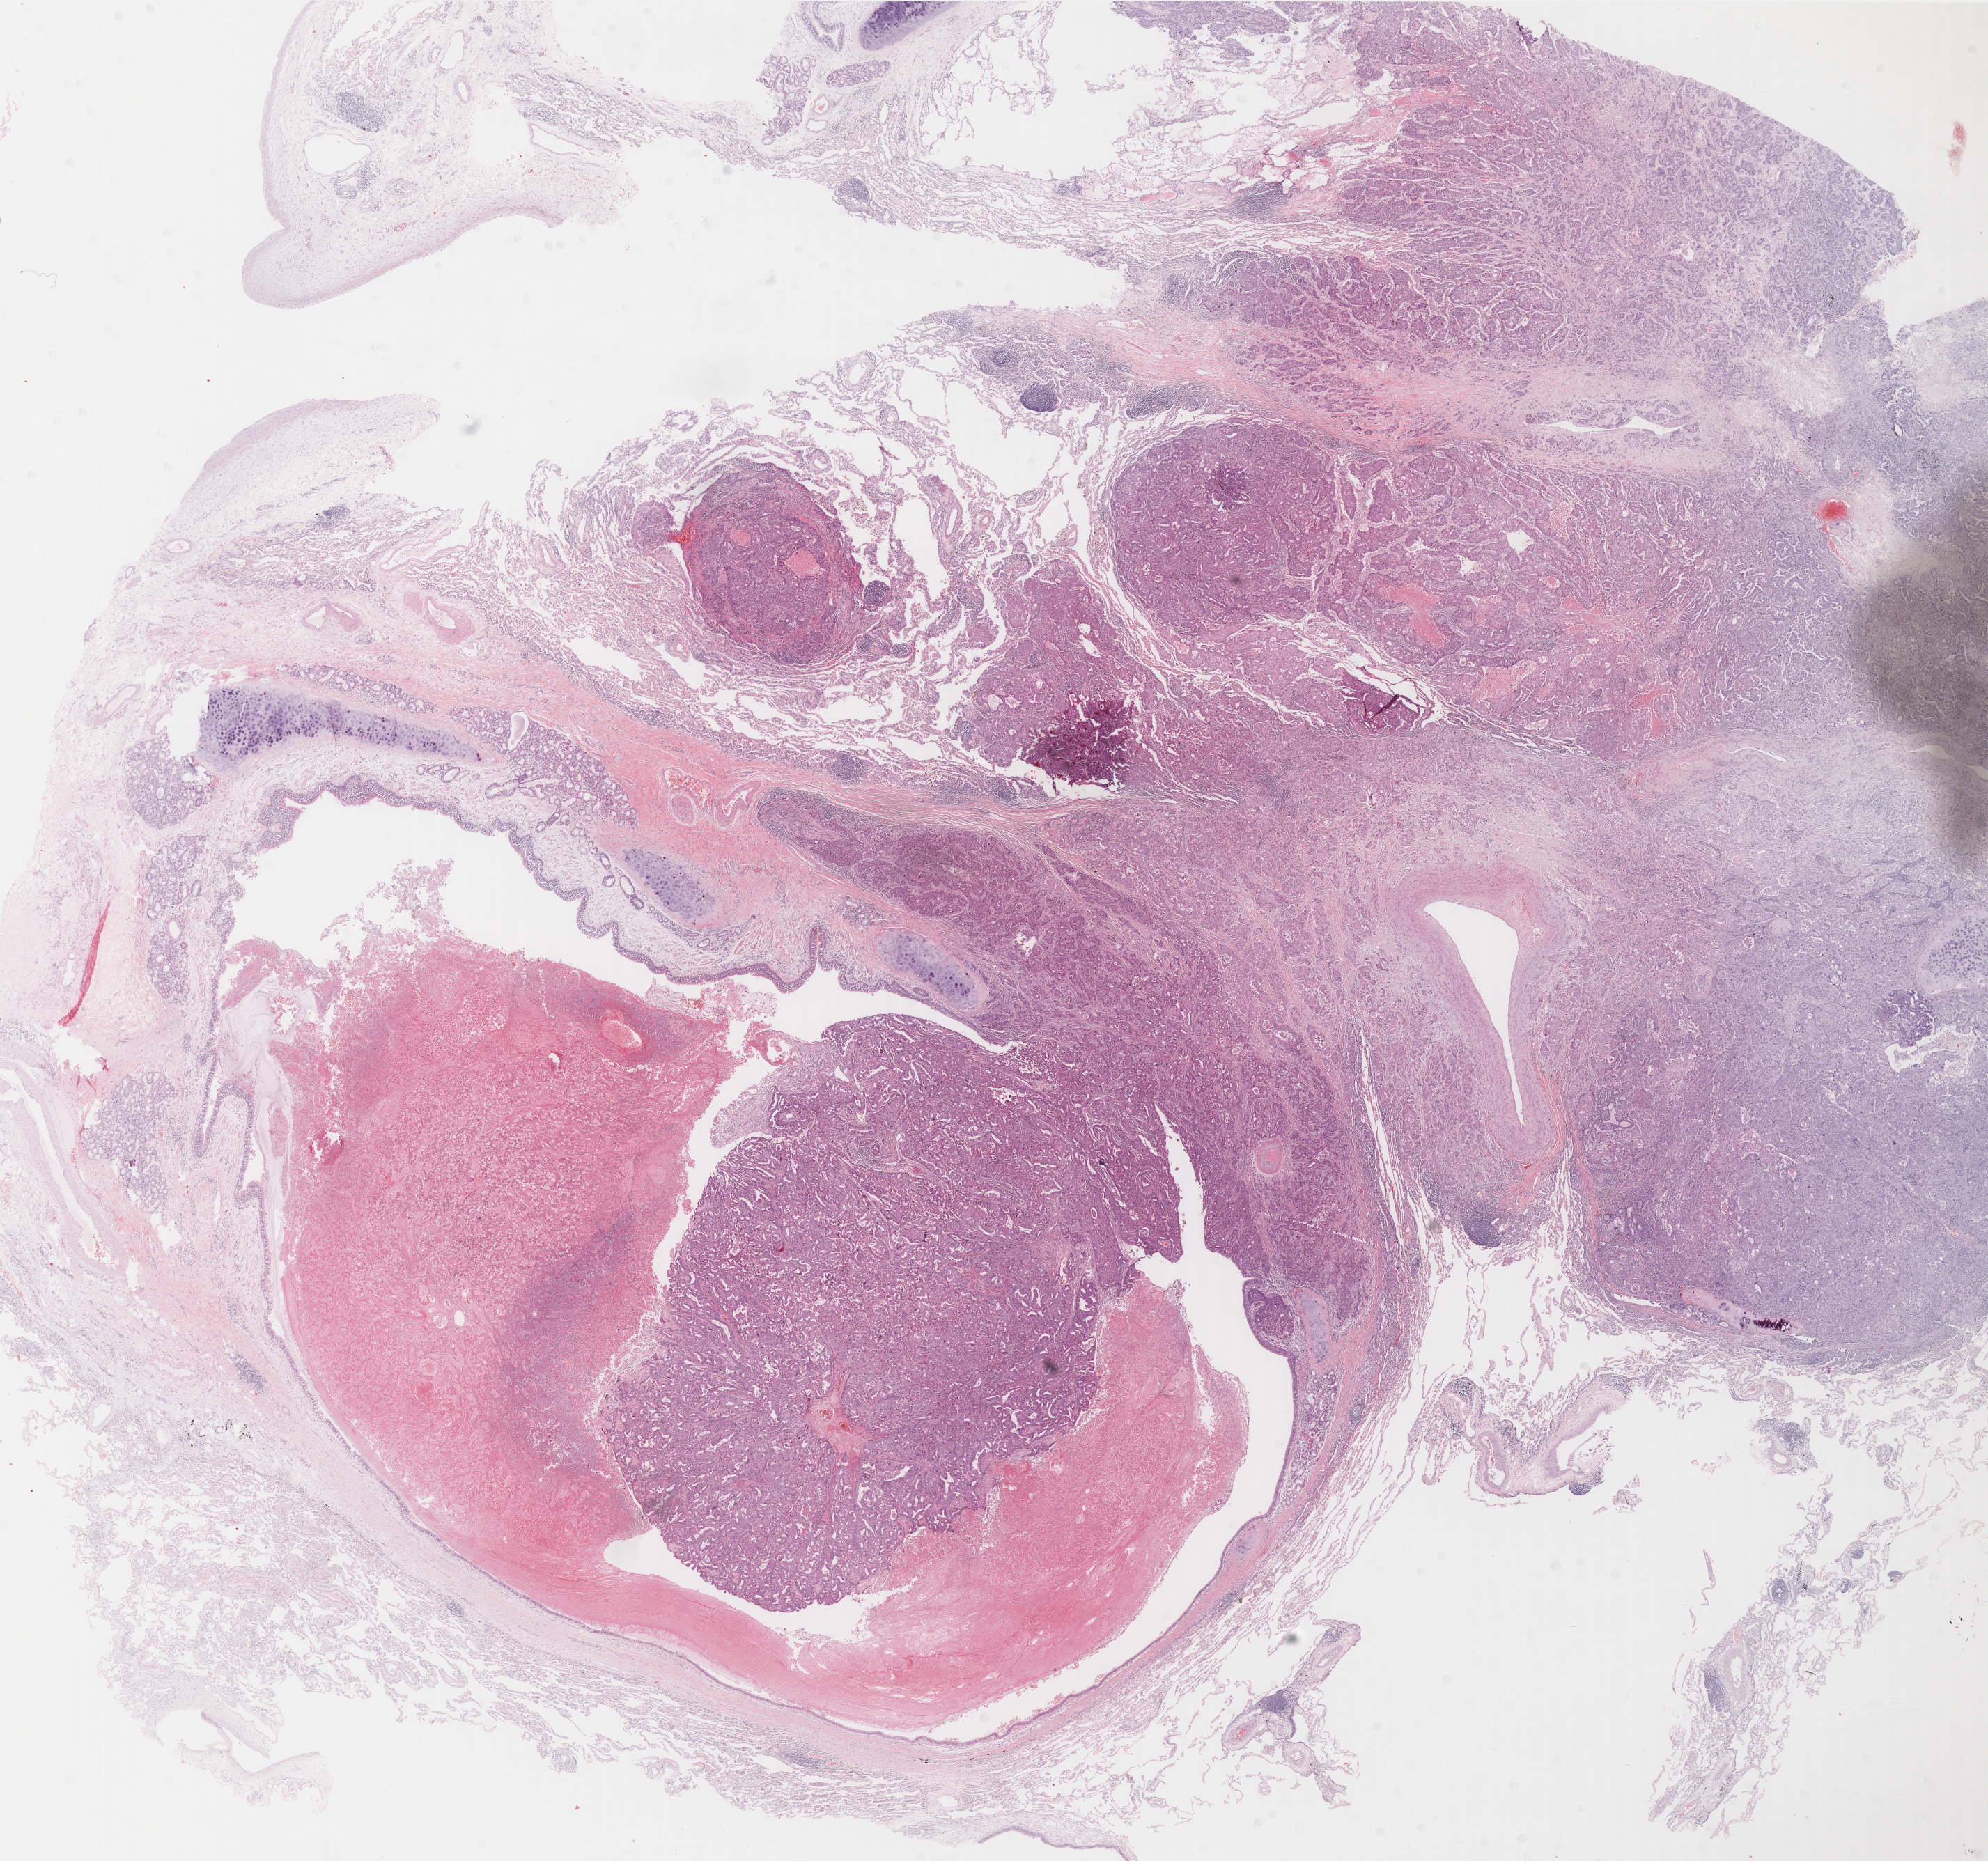
Digitized Hematoxylin and eosin (H&E) stained tissue section (whole slide), a low-resolution overview of the entire scanned area, about 23.0 x 21.5 mm; FFPE section; sample: primary tumour, lung. Patient: female, age at initial diagnosis 65 years.
• laterality: right
• AJCC pathologic stage: IB (6th edition)
• histologic diagnosis: Adenocarcinoma, NOS (lower lobe, lung)